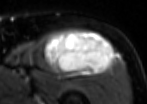
MRI of an extremity soft-tissue mass, one axial slice. Position 65 of 85 along the scan axis. T2-weighted fat-saturated. MR volume resampled by the dataset authors to the PET/CT grid (not the native acquisition matrix). 147 × 104 image matrix, field of view 144 × 102 mm. Male patient. From the clinical record (not read from this slice): histological type: extraskeletal osteosarcoma; grade: high; site of the primary tumour: thigh.
Outlined on this slice (expert contour drawn on MRI and transferred to this co-registered scan by the dataset authors):
- gross tumour volume (mass): bounding box <44,30,114,75> (left, top, right, bottom; pixels)